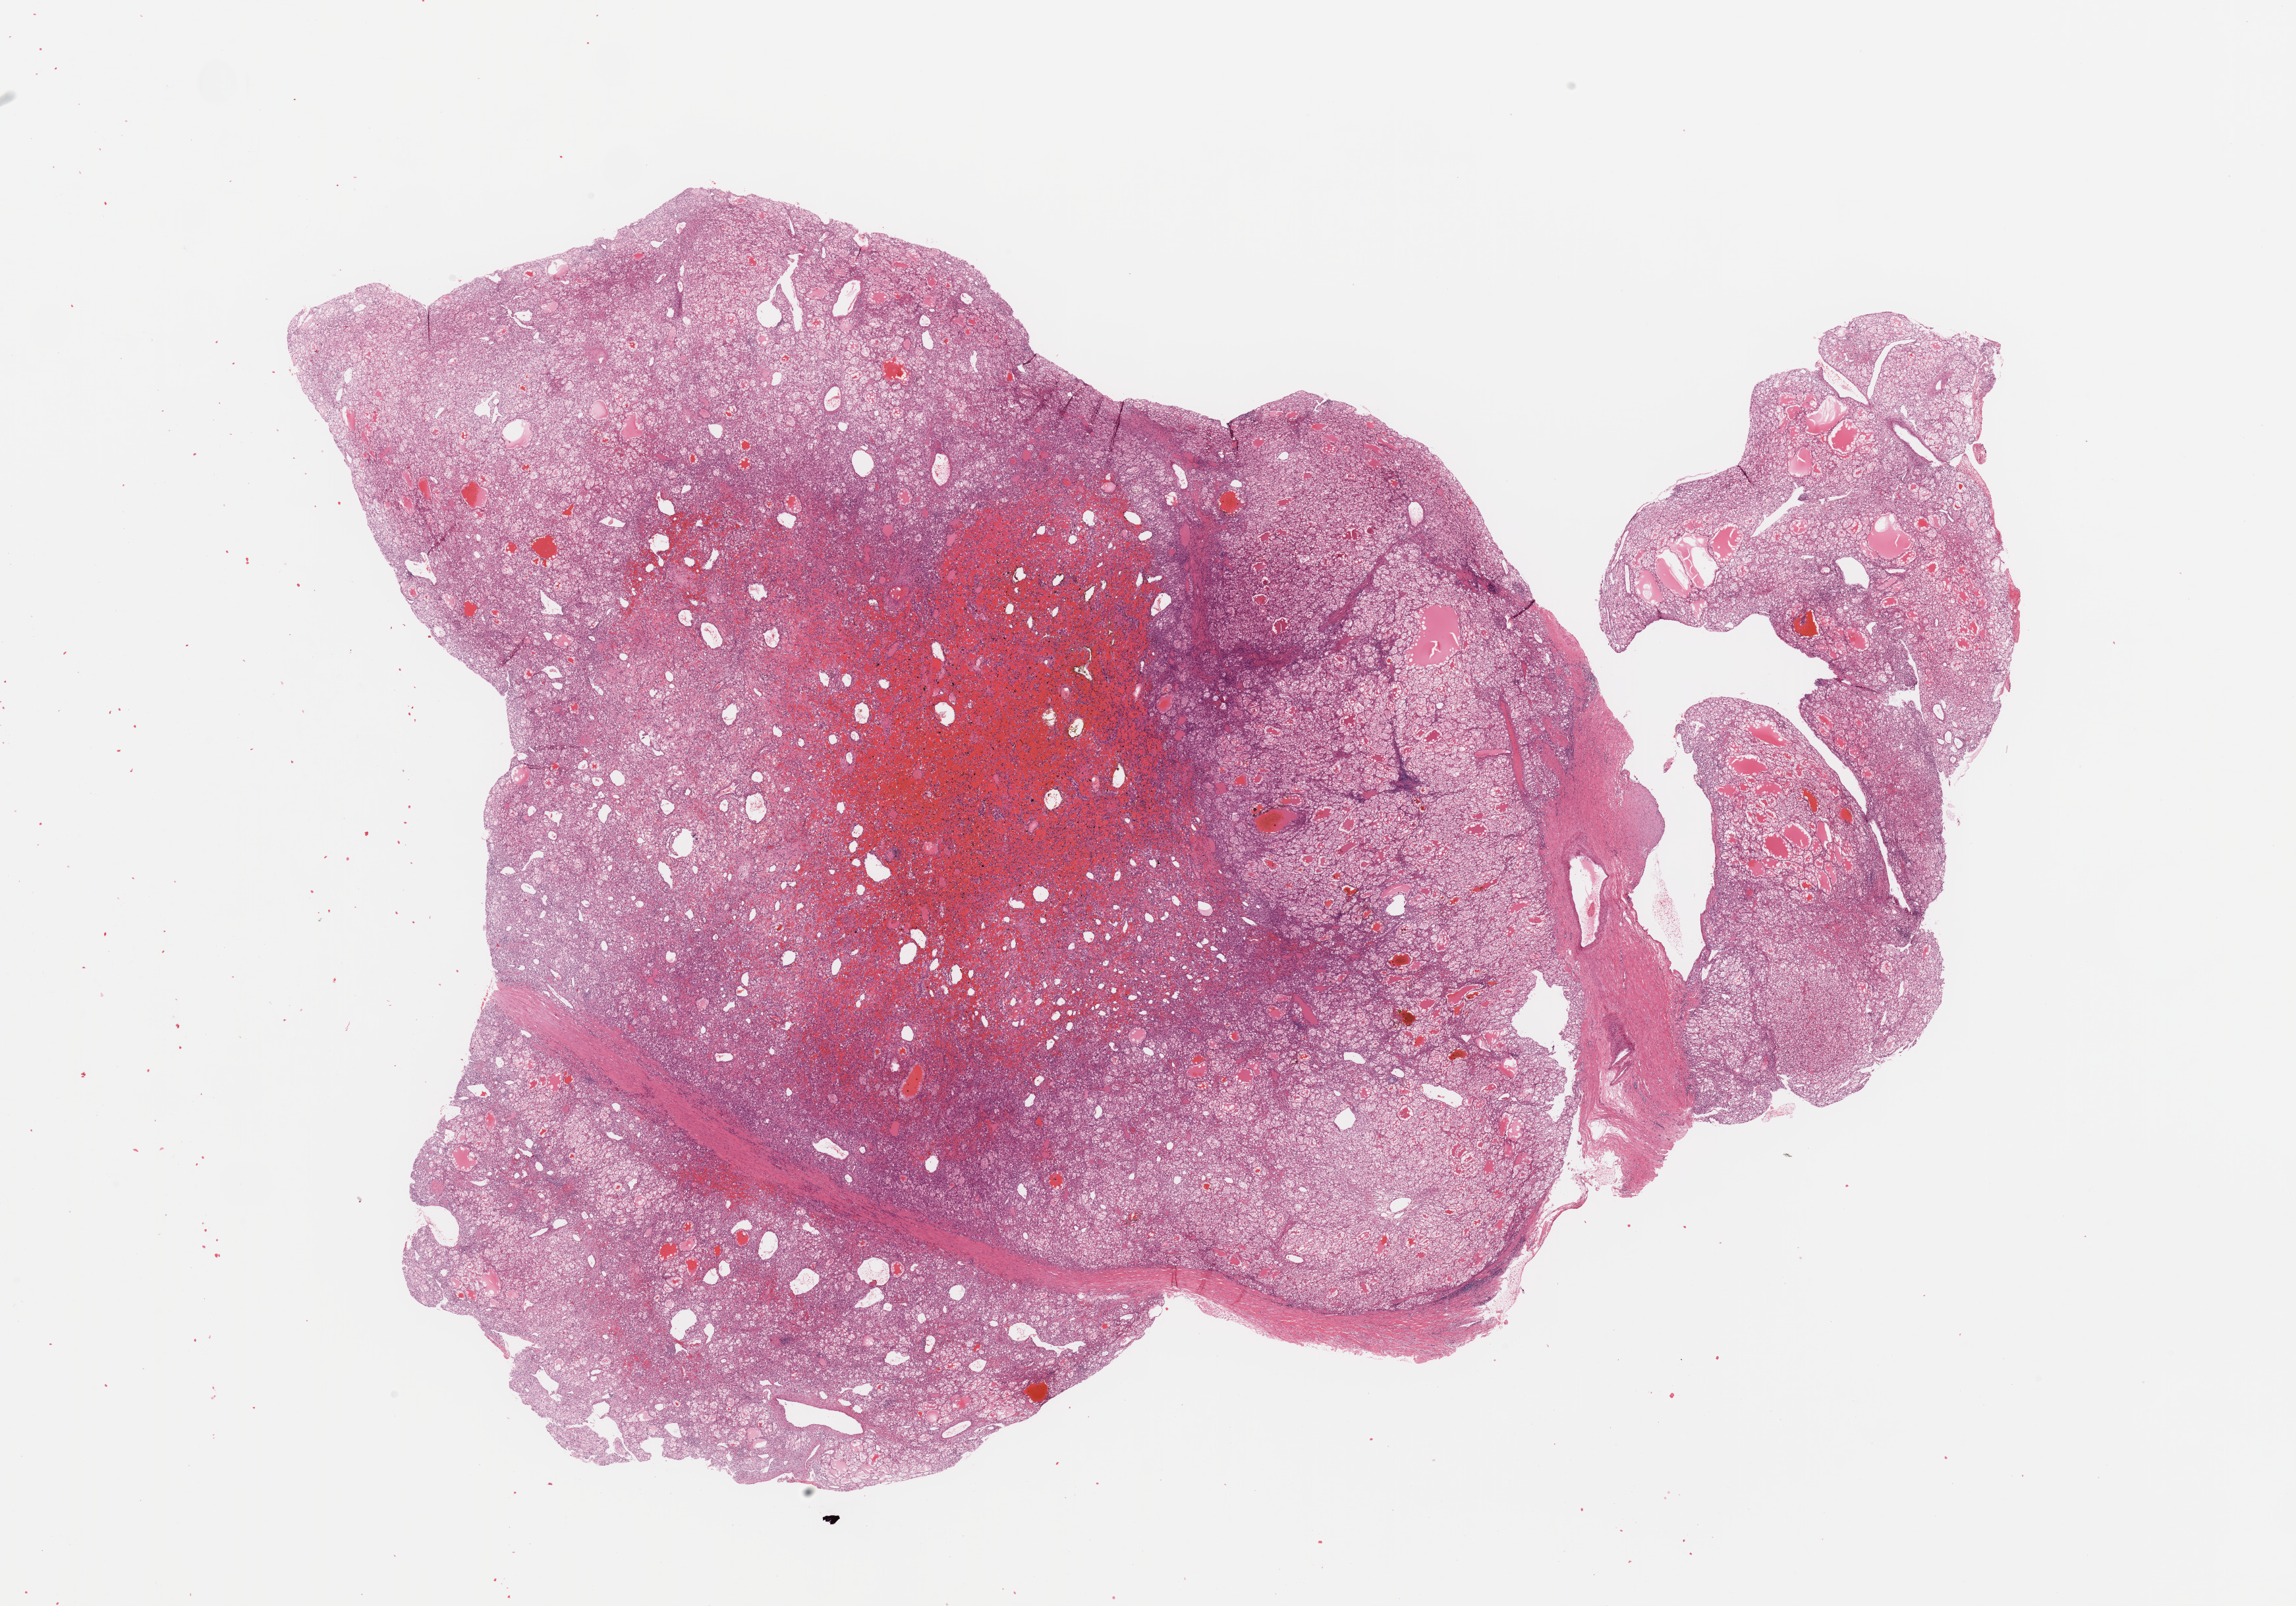
Digitized H&E tissue section (whole slide) — a low-resolution overview of the entire scanned area, about 27.6 x 19.3 mm (acquisition: 20x scan), tumour tissue sample, sampled site: kidney. Patient: female, age 42 years. Histologic grade: G2 (moderately differentiated). Composition of this section per pathologist review: tumour nuclei 85%, necrosis 0%.
Diagnosis: Renal cell carcinoma, NOS.